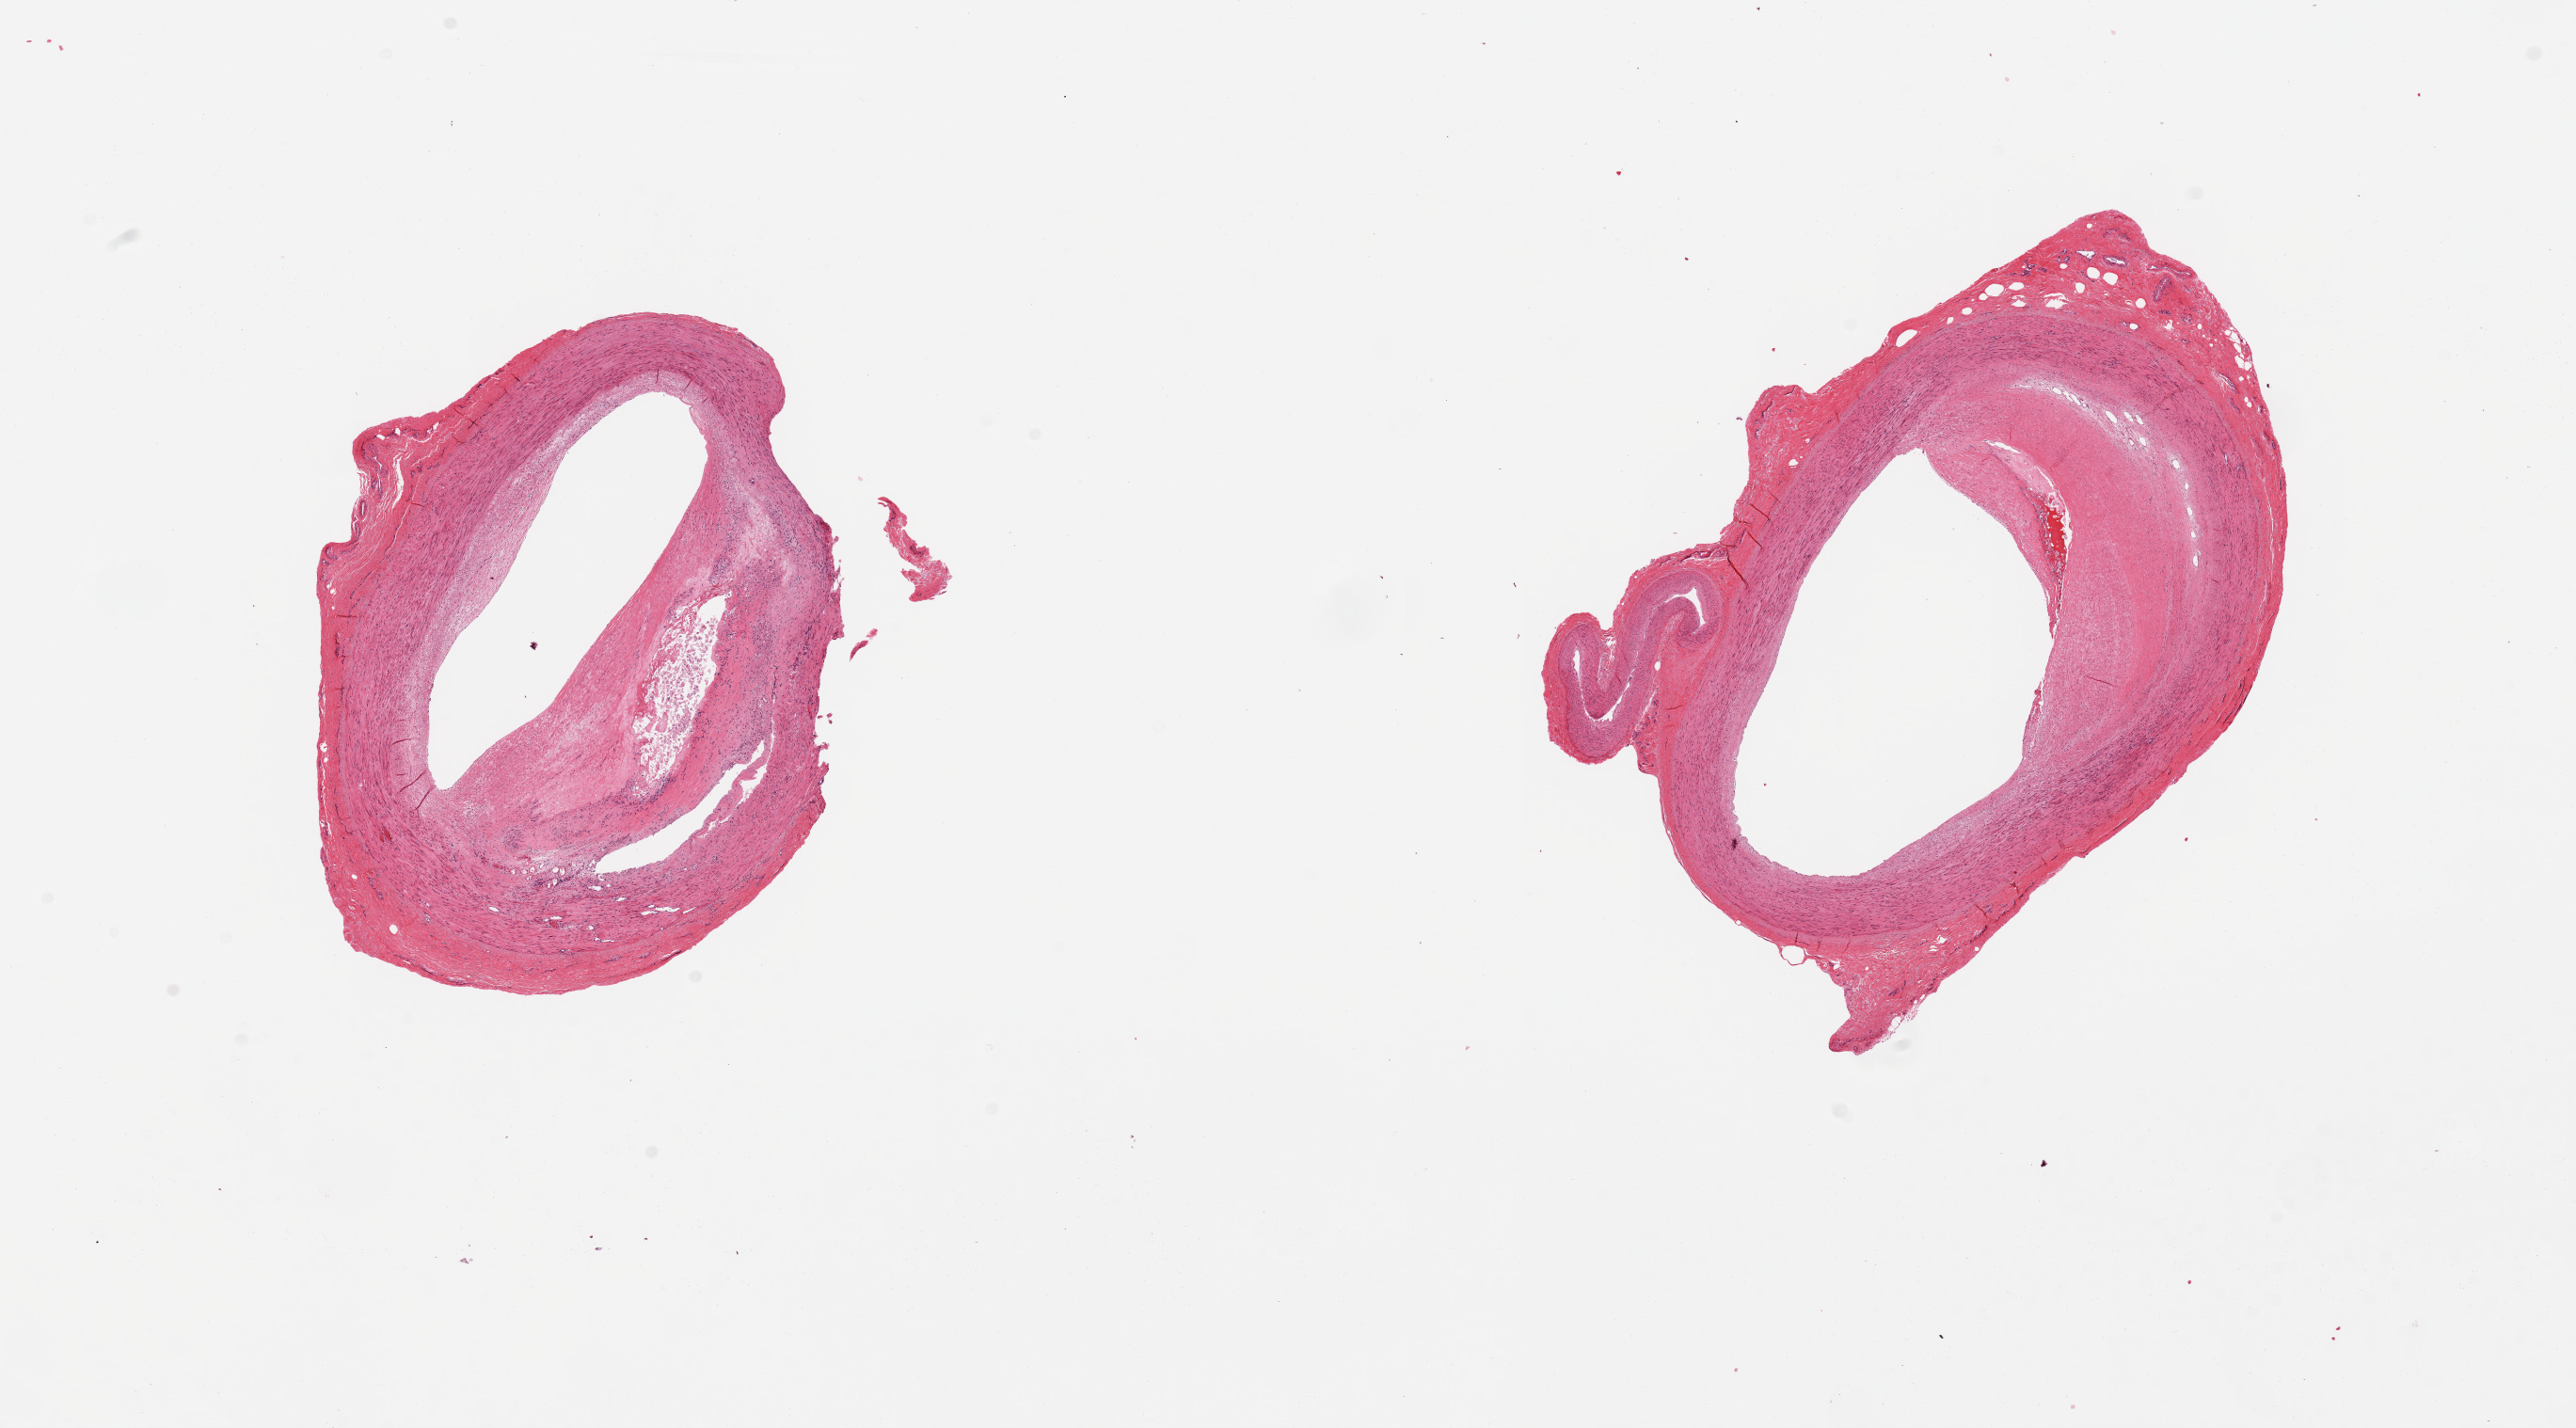
Haematoxylin and eosin whole-slide image, brightfield — a low-resolution overview of the entire scanned area, about 21.7 x 12.0 mm (from a 20x scan), PAXgene-fixed paraffin-embedded (PFPE) section, sampled site (target tissue): tibial artery, donor tissue sample.
- pathologist's review note for this sample: 2 pieces; eccentric fibrofatty plaque